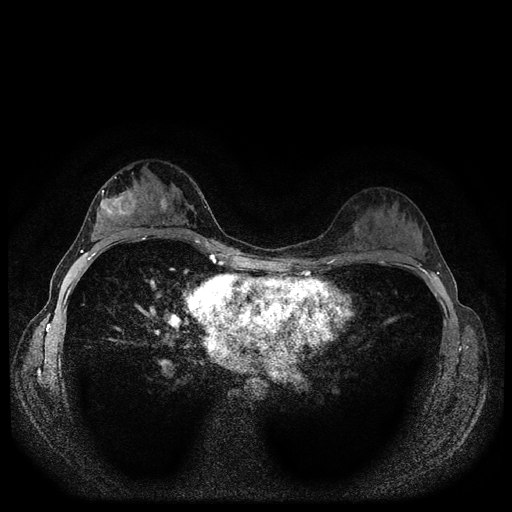
Breast MRI (dynamic contrast-enhanced, multi-phase), one axial slice. Position 65 of 116 along the scan axis. Dynamic contrast-enhanced series, time point 2 of 5 at this slice position (early post-contrast). 1.5 T. TE 2.7 ms, TR 5.4 ms. 2 mm slice thickness. 512 × 512 image matrix, field of view 320 × 320 mm. Female patient, age 29 years.
Outlined on this slice (semi-automatically segmented with operator editing):
- breast lesion (labelled benign in the annotation): box from (x=159, y=196) to (x=170, y=215) px
- breast lesion (labelled 'tumour' in the annotation; benign lesions carry a separate 'benign' label): (x=96, y=187)–(x=139, y=222)